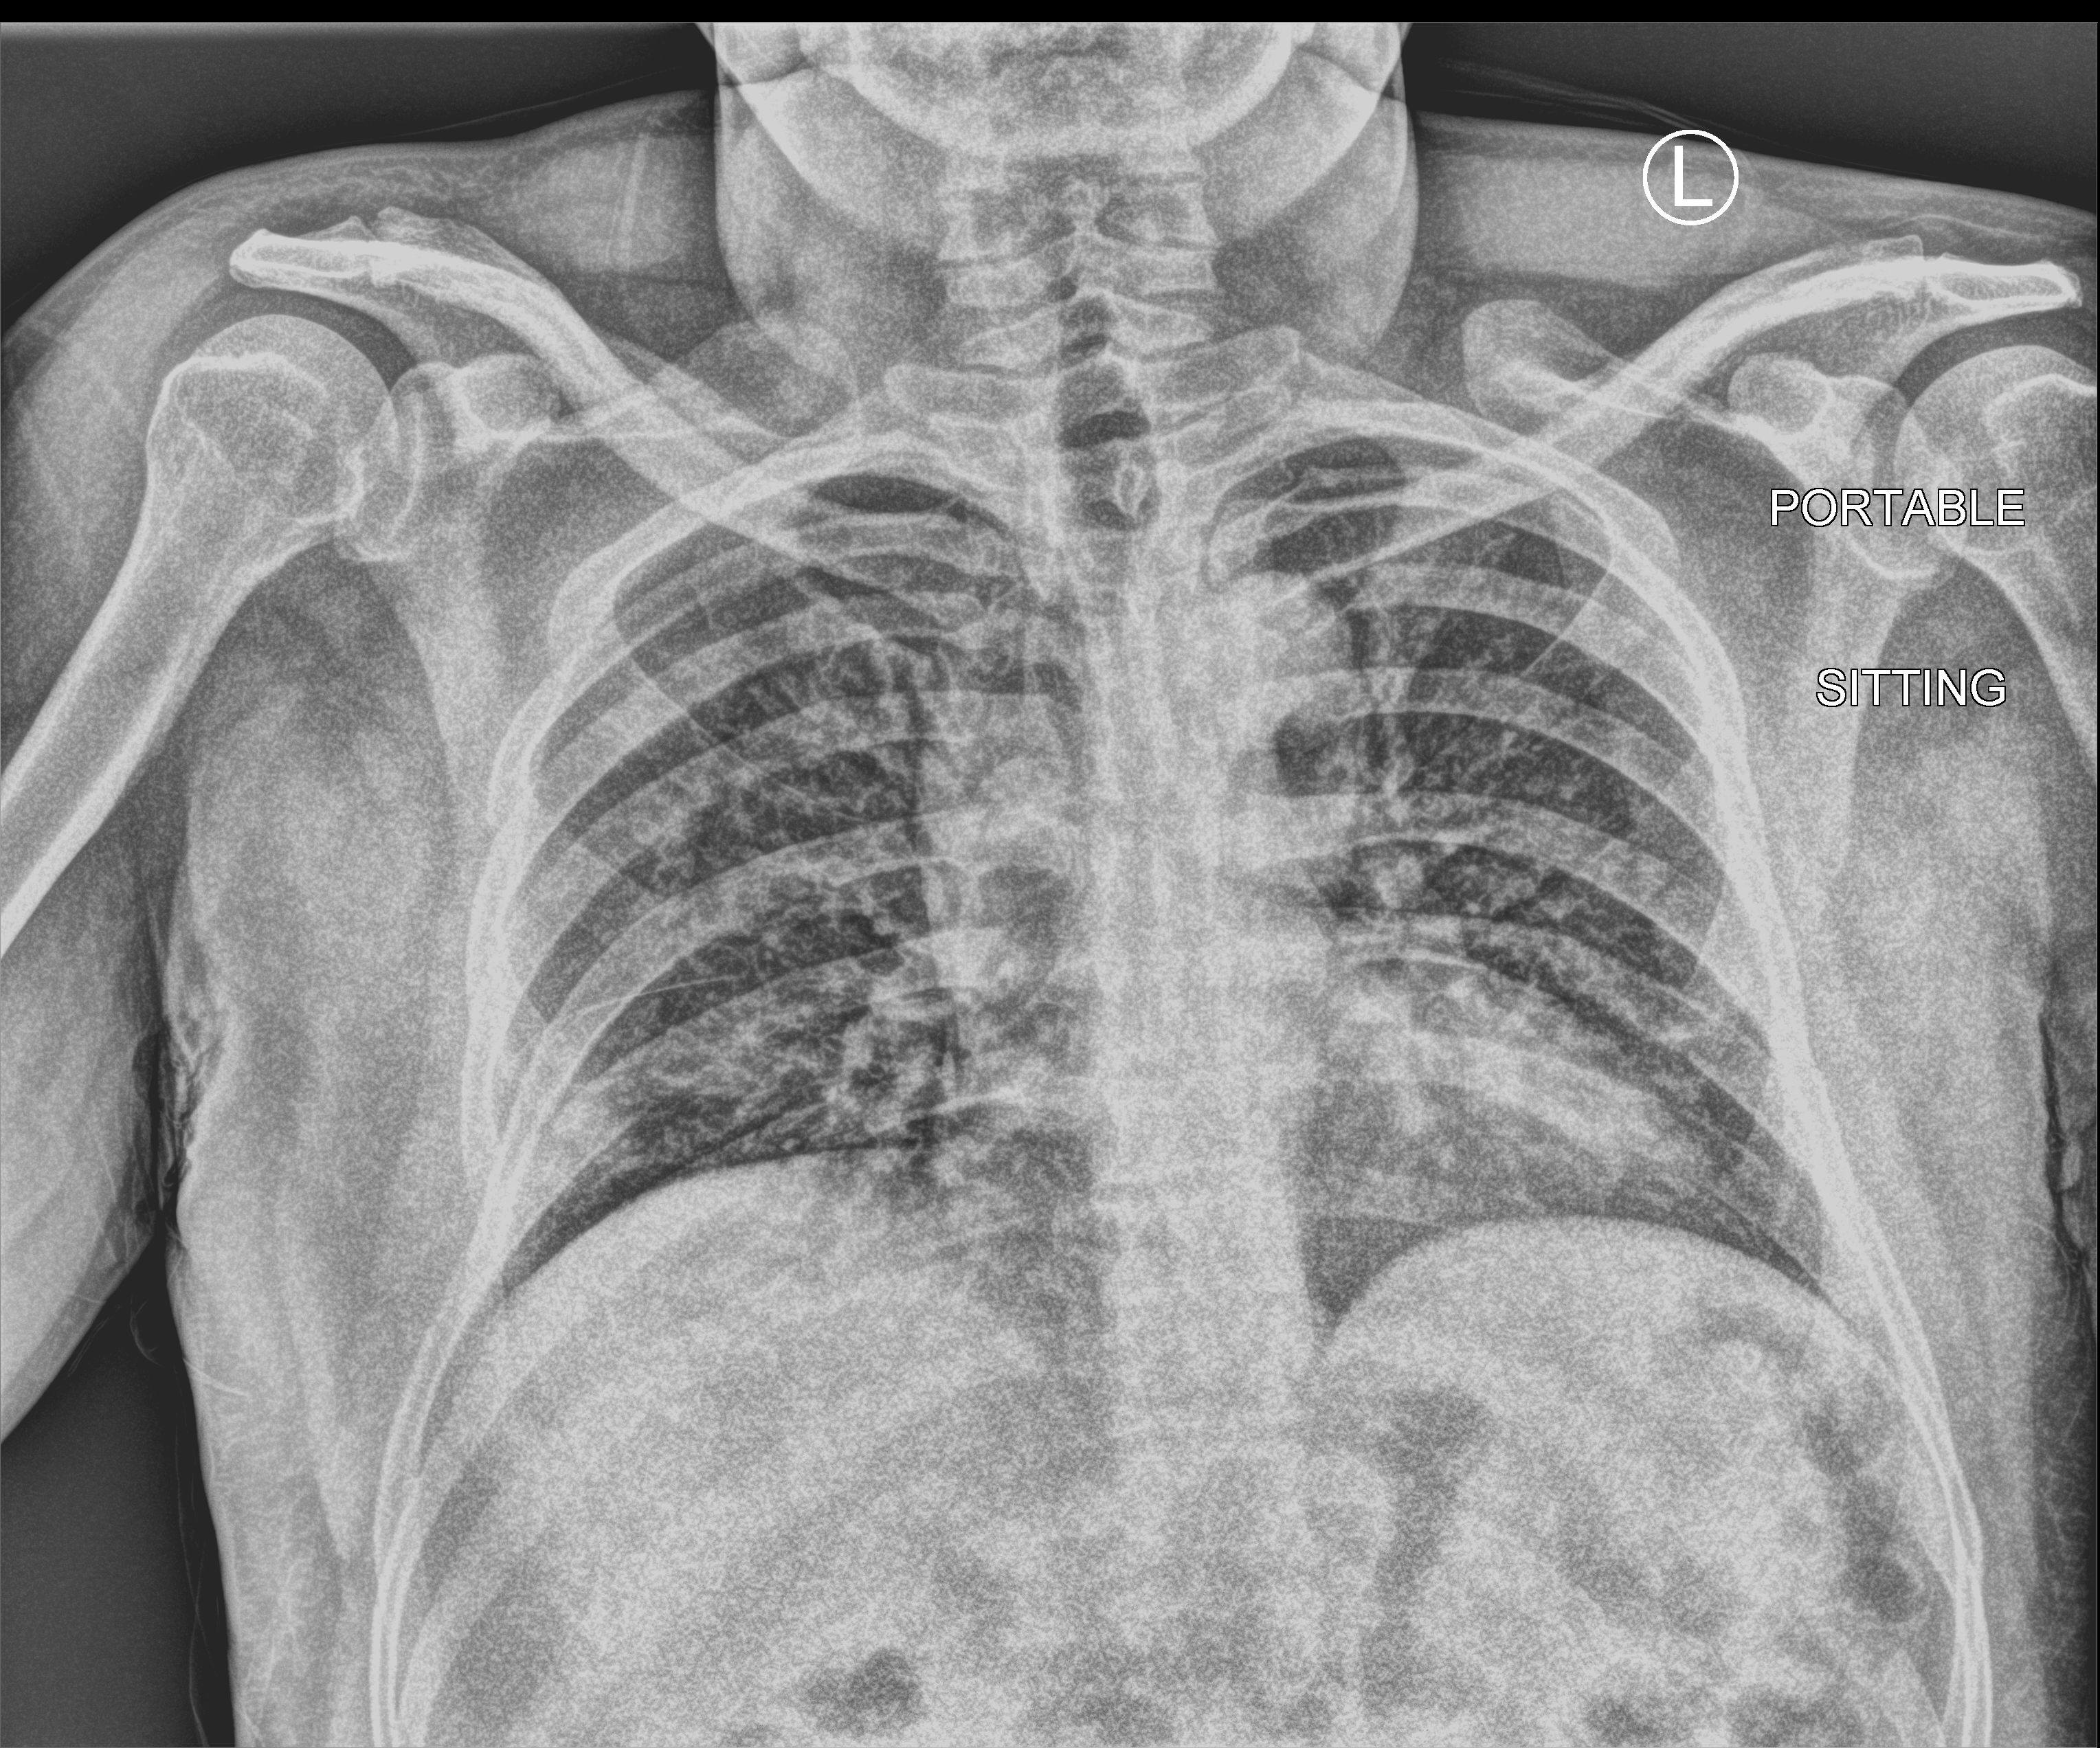
Chest X-ray (portable); anteroposterior (AP) projection. Patient hospitalised with COVID-19; male, aged 18–59 years.
Hospital-stay facts (about this admission, not read from this image; timing relative to this image not recorded):
- admitted to intensive care during this hospital stay: no